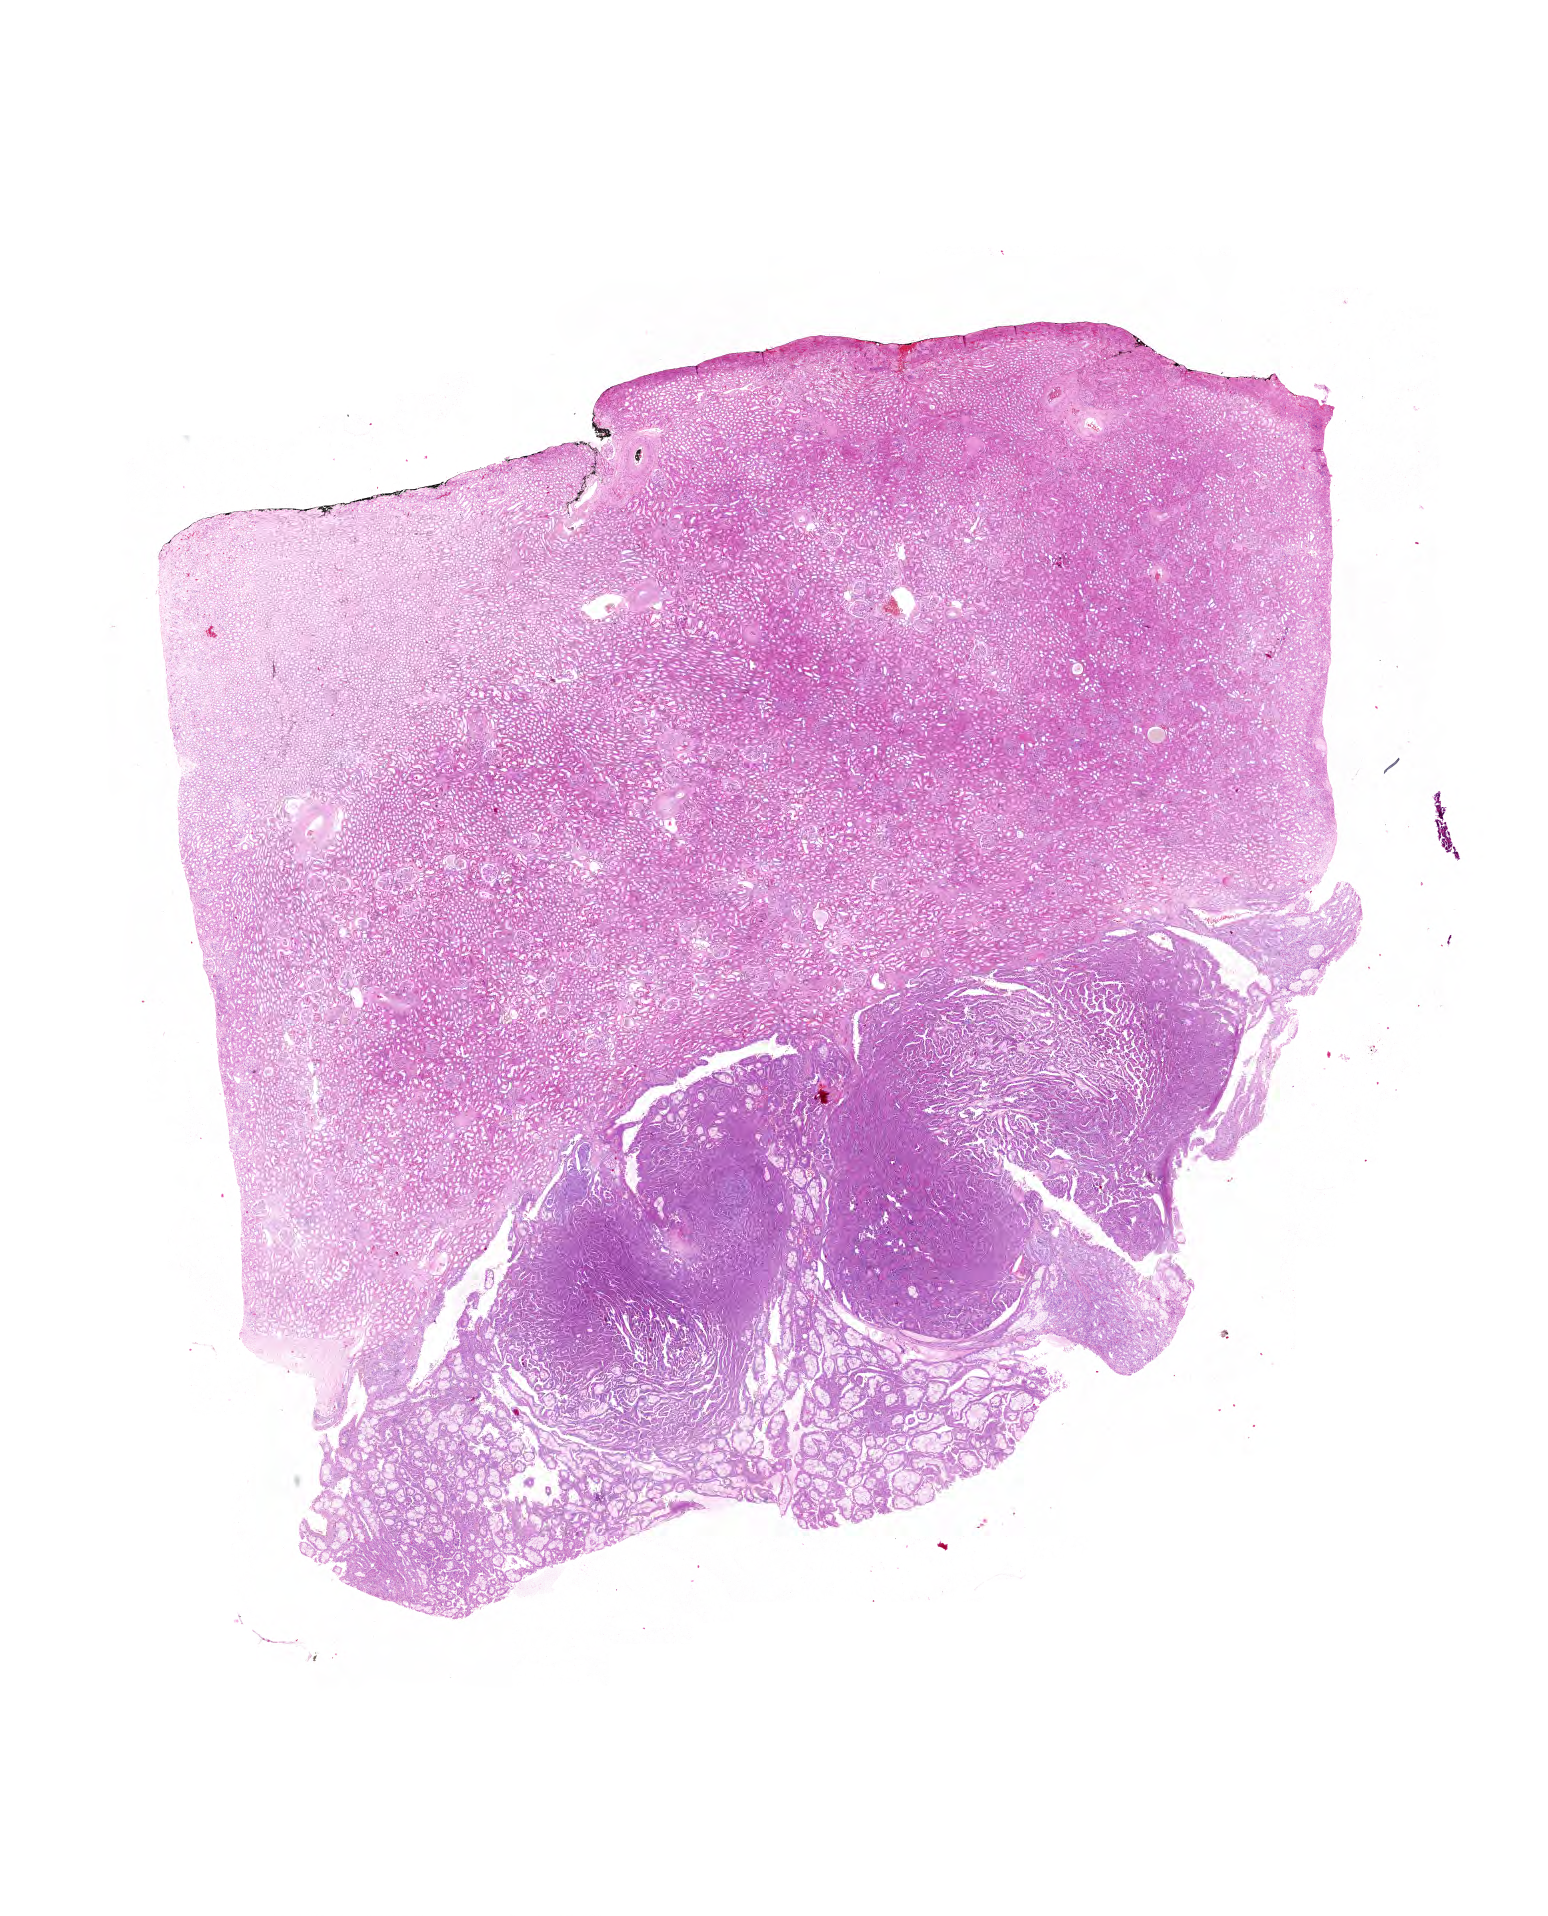
H&E-stained whole-slide image — whole scanned area (about 19.3 x 23.8 mm) shown as a low-resolution overview; formalin-fixed paraffin-embedded (FFPE) diagnostic section; primary tumour sample from the kidney. Male patient; age at initial diagnosis 64 years.
Laterality: right. Histologic diagnosis: Papillary adenocarcinoma, NOS.